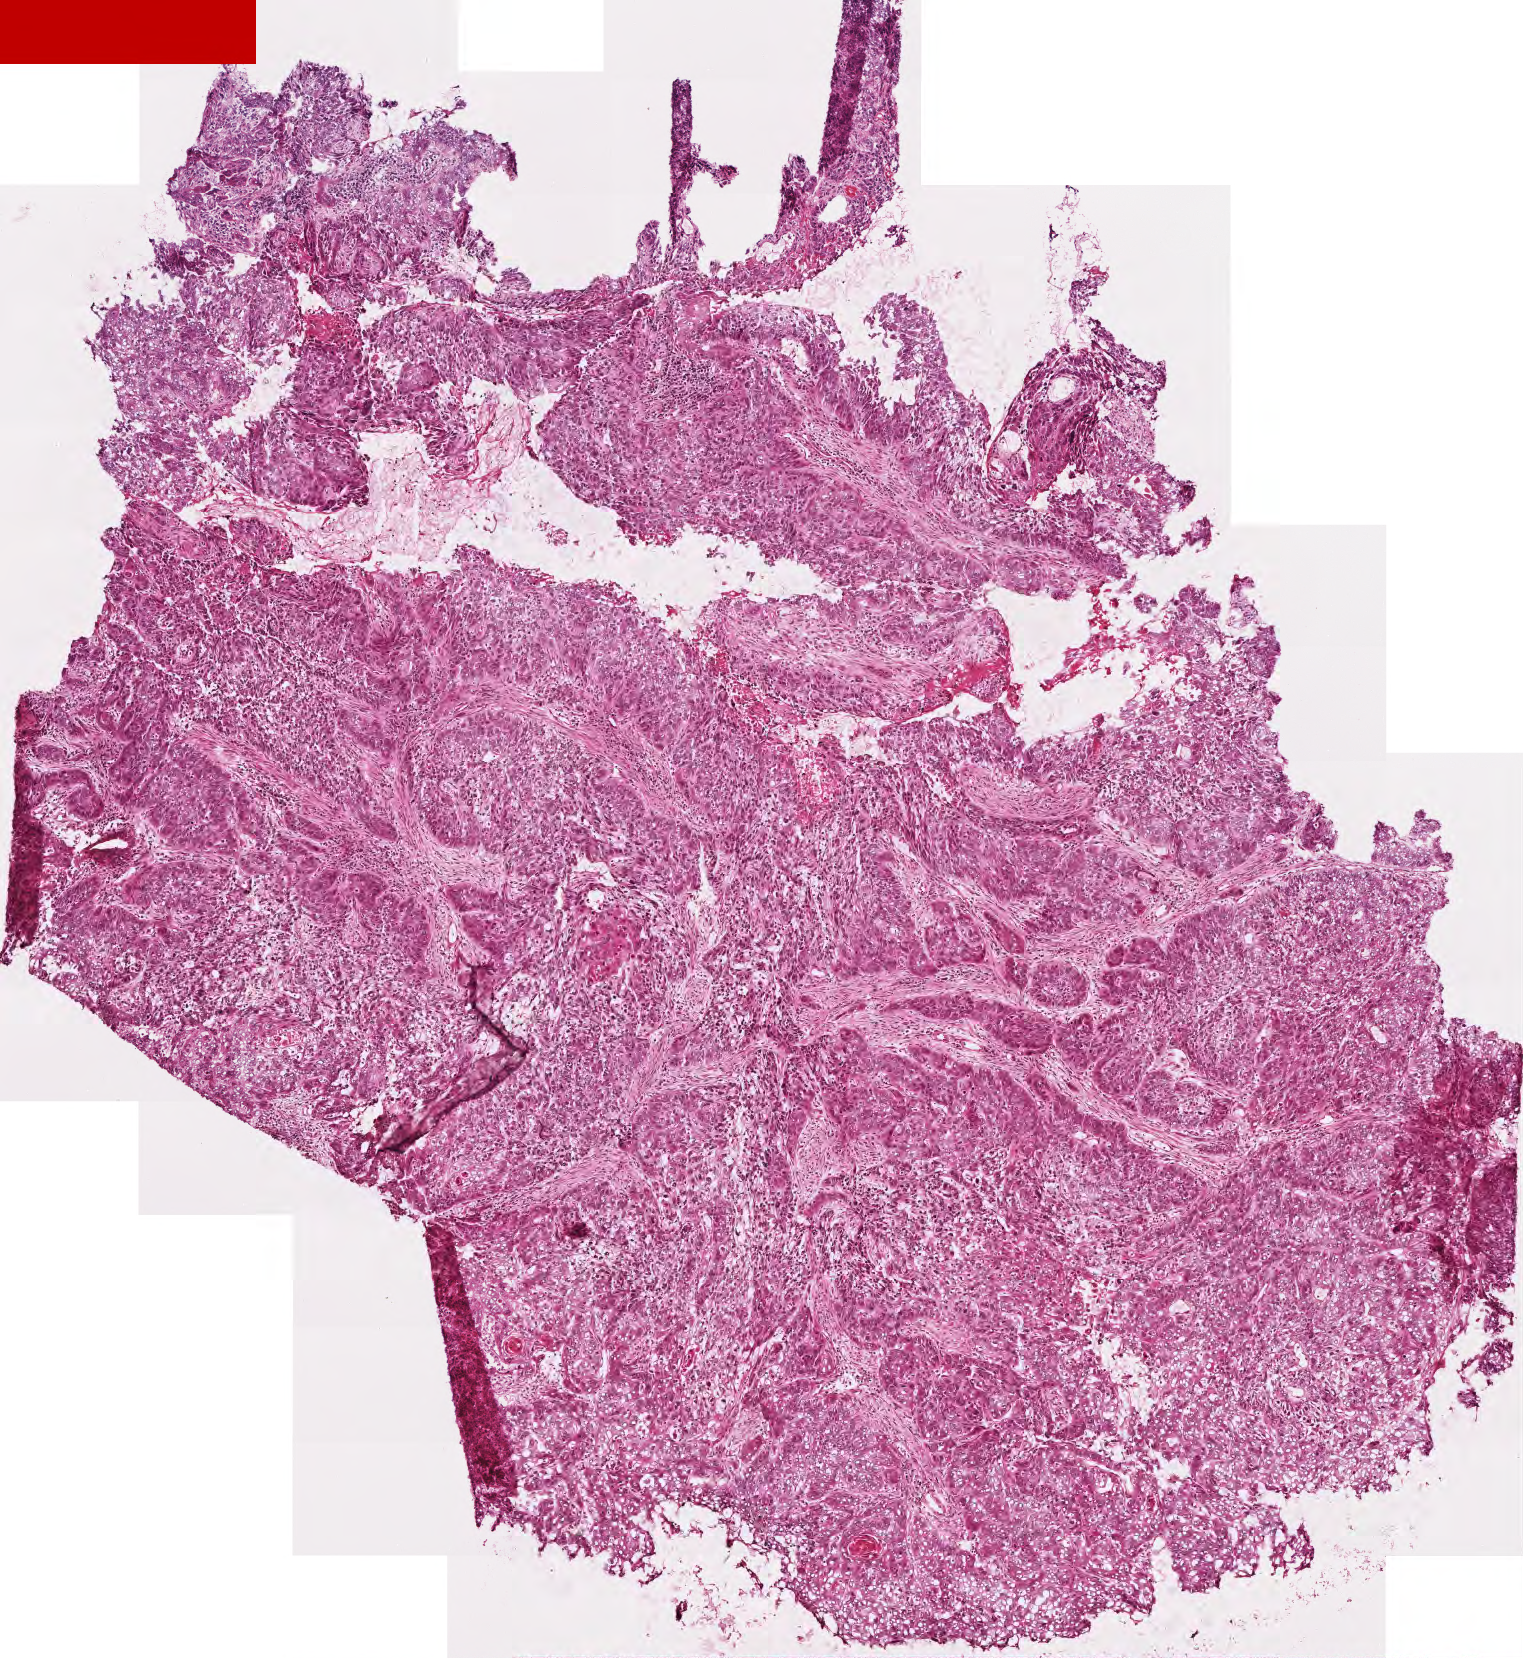
Whole-slide histology image, H&E — whole scanned area (about 3.0 x 3.3 mm) shown as a low-resolution overview. Frozen section from the top of the tissue portion. Sample: primary tumour, head and neck. Female patient; age at initial diagnosis 72 years. Histologic grade: G2 (moderately differentiated). Slide review estimates, as recorded: tumour cells 90%, tumour nuclei 90%, normal cells 0%, stromal cells 10%, necrosis 0%. Inflammatory infiltration, as recorded: lymphocyte infiltration 5%.
• diagnosis: Squamous cell carcinoma, NOS